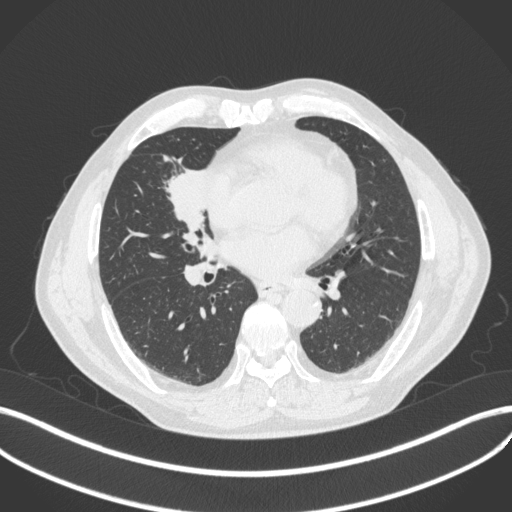
Chest CT, one axial slice. Position 186 of 429 along the scan axis. Reconstruction kernel B31f. Lung window (W 1500 / L -600 HU). 1 mm slice thickness. 512 × 512 image matrix, field of view 400 × 400 mm. Patient: male, 61 years. From the clinical record (not read from this slice): clinical TNM (as recorded): T2b N1 M0.
Annotated regions visible in this slice (rectangle marked by the reading radiologist):
- lung tumour (recorded histology: squamous cell carcinoma): bounding box <161,156,213,233> (left, top, right, bottom; pixels)